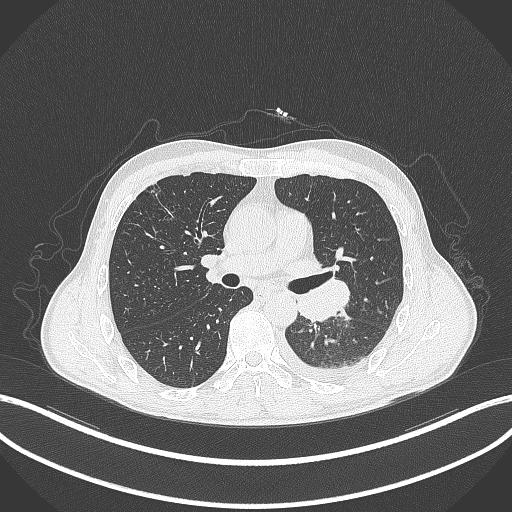
Chest CT, one axial slice. Position 185 of 295 along the scan axis. Reconstruction kernel B70f. Lung window (W 1500 / L -600 HU). 1 mm slice thickness. 512 × 512 image matrix. Male patient, age 47 years. From the clinical record (not read from this slice): clinical TNM (as recorded): T3 N1 M1c.
Outlined on this slice (rectangle marked by the reading radiologist):
- lung tumour (recorded histology: small cell carcinoma): bounding box (x1, y1, x2, y2) in pixels: (295, 277, 353, 322)